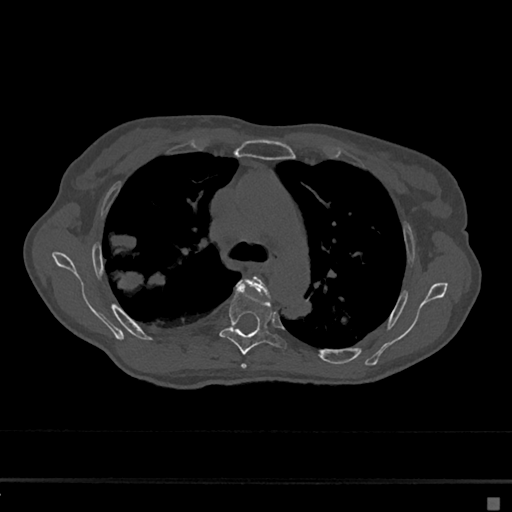
CT including the spine, one axial slice; position 466 of 797 along the scan axis; reconstruction kernel Br40s/3; 120 kVp; bone window (W 1800 / L 400 HU); 0.5 mm slice thickness; 512 × 512 image matrix. Female patient, age 68 years. From the clinical record (not read from this slice): primary cancer: renal.
Annotated regions visible in this slice (semi-automatic segmentation, software-assisted and operator-edited):
- T4 vertebra: bounding box [x1, y1, x2, y2] px = [237, 276, 271, 369]
- T5 vertebra: [220, 287, 287, 355]